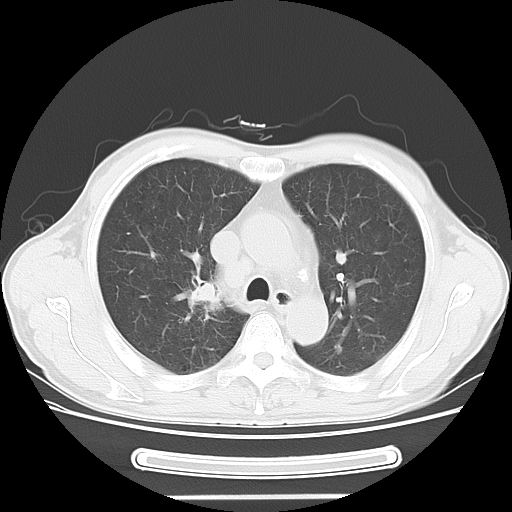
Chest CT, one axial slice. Slice 34 of 51 in the series (ordered by position). Reconstruction kernel LUNG. Lung window (W 1500 / L -600 HU). 512 × 512 image matrix, field of view 350 × 350 mm. Male patient, age 57 years. From the clinical record (not read from this slice): clinical TNM (as recorded): T2 N3 M1b.
Outlined on this slice (bounding box drawn by a radiologist):
- lung tumour (recorded histology: adenocarcinoma): bounding box [x1, y1, x2, y2] px = [184, 279, 222, 314]